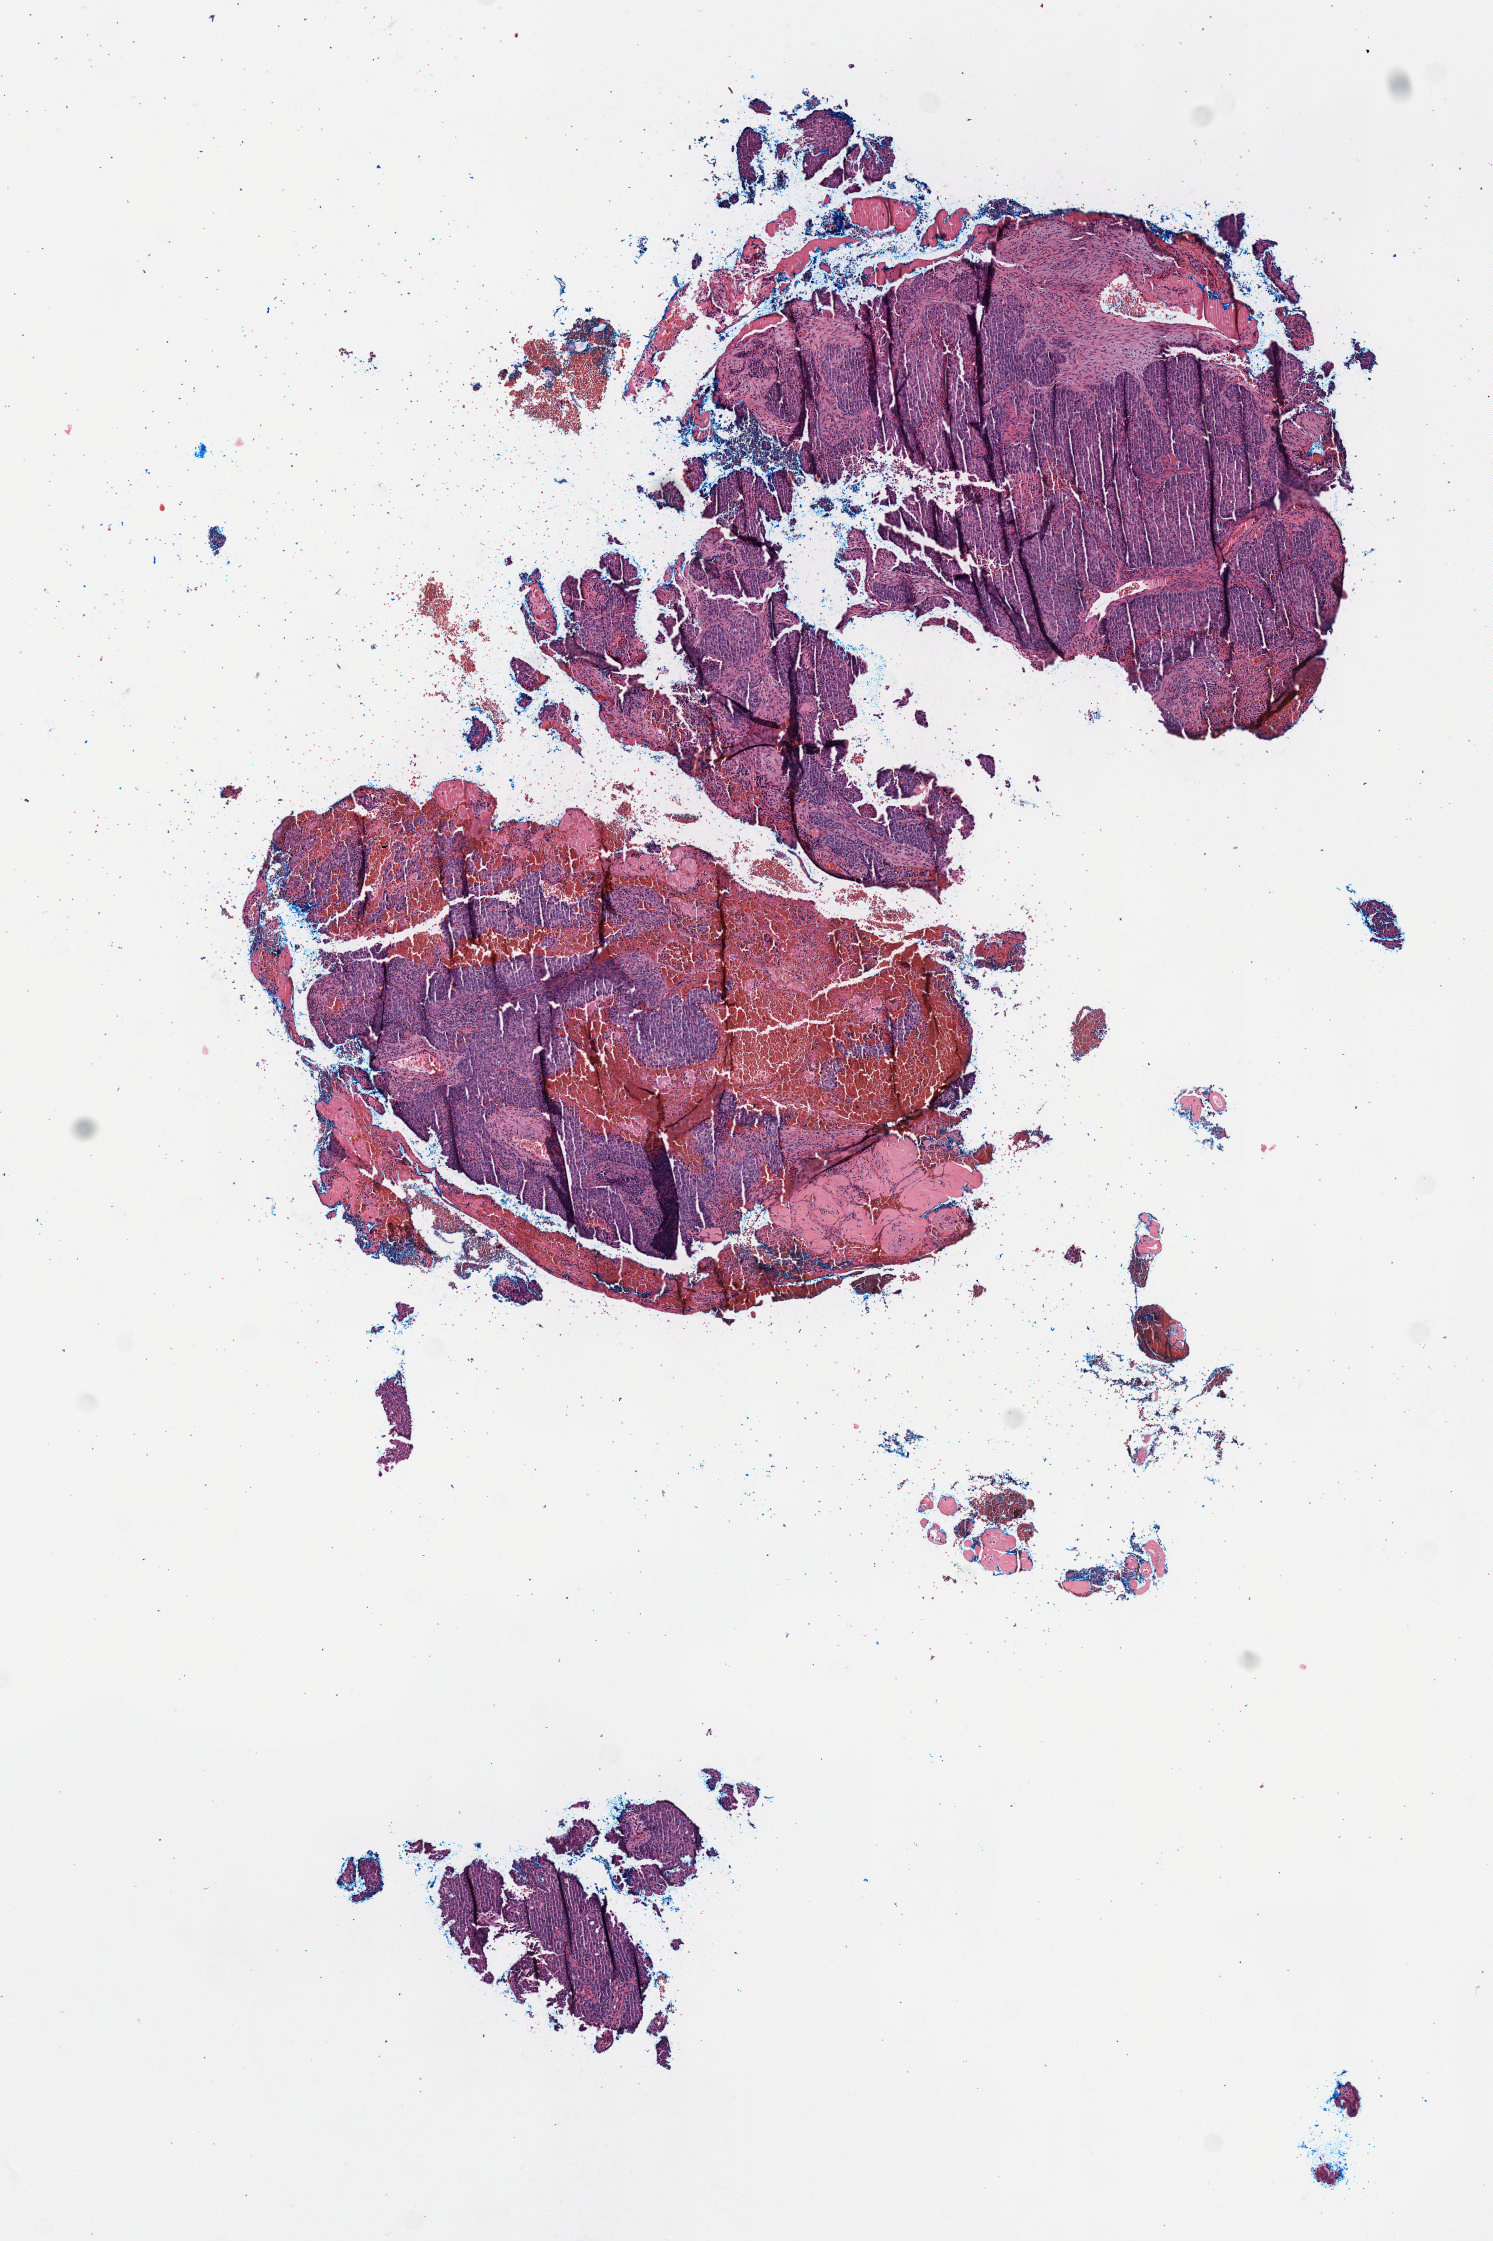
Digitized H&E tissue section (whole slide) — whole scanned area (about 6.0 x 9.1 mm) shown as a low-resolution overview. Formalin-fixed paraffin-embedded (FFPE) diagnostic section. Sample: primary tumour, cervix. Female, age 55 years at initial diagnosis. Histologic grade: GX (grade cannot be assessed).
• FIGO stage: IIB
• pathologic diagnosis: Squamous cell carcinoma, NOS (cervix uteri)